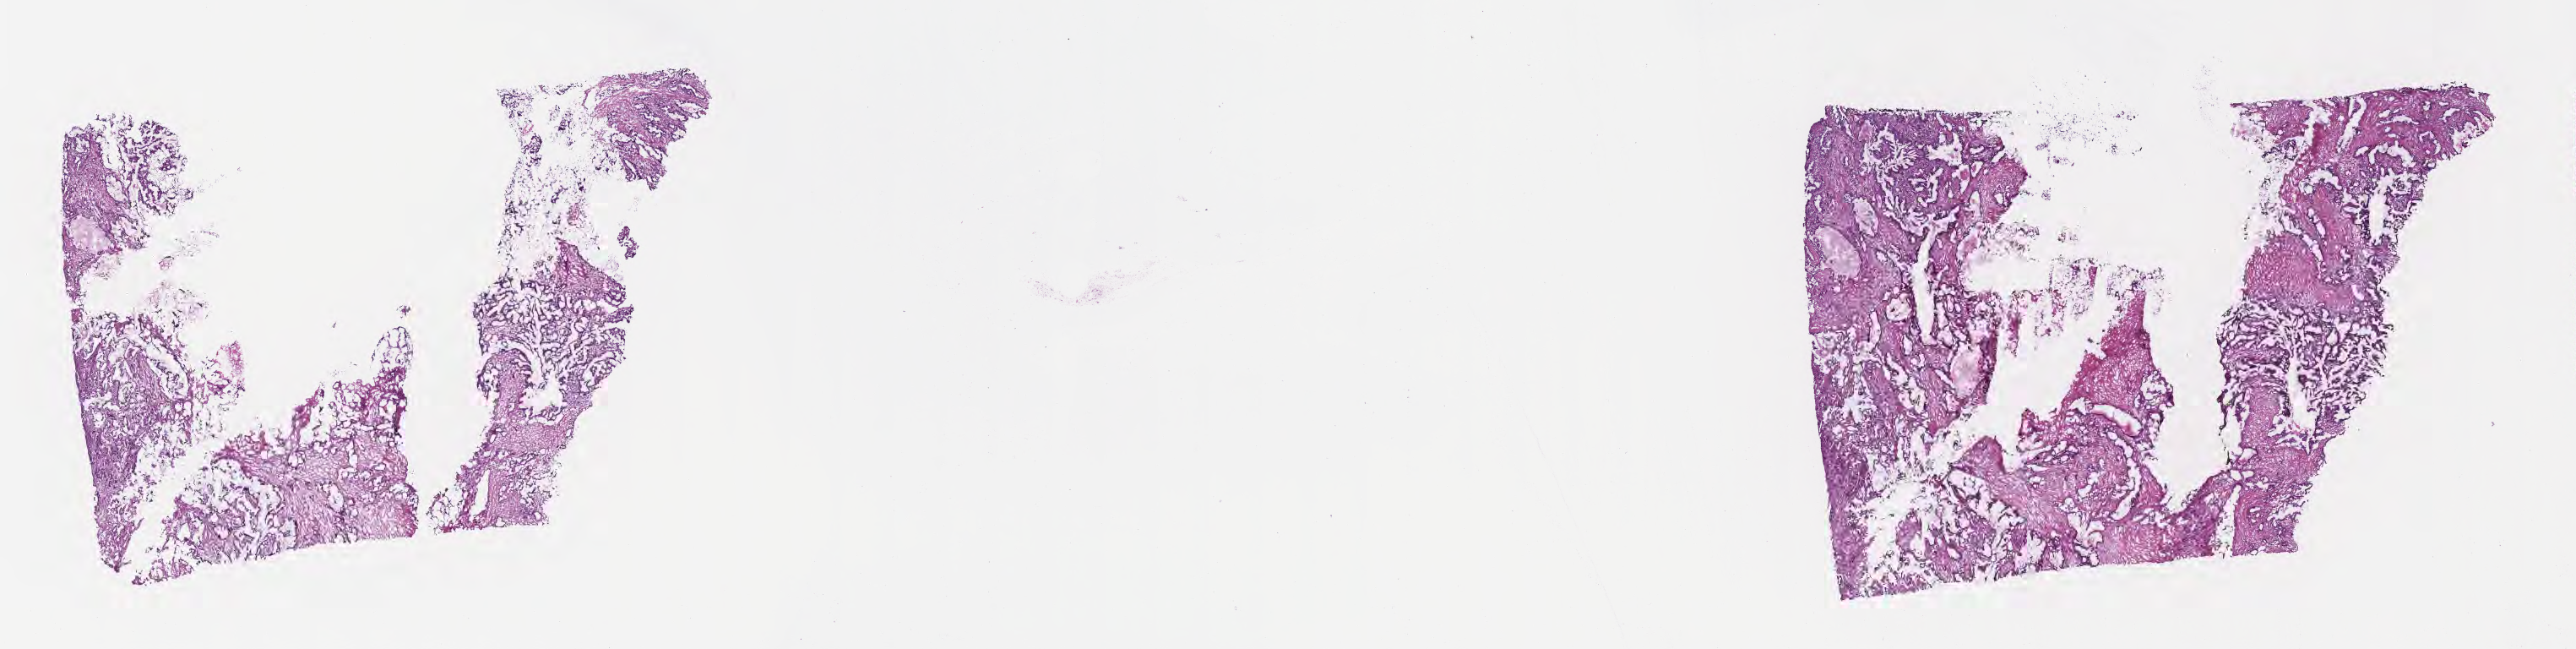
Digitized hematoxylin and eosin (H&E)-stained section — a low-resolution overview of the entire scanned area, about 24.7 x 6.2 mm. Cryosection. Specimen: primary tumor. Anatomic site: head of pancreas. Male, age 71 years at initial diagnosis.
Diagnosis: Infiltrating duct carcinoma, NOS.